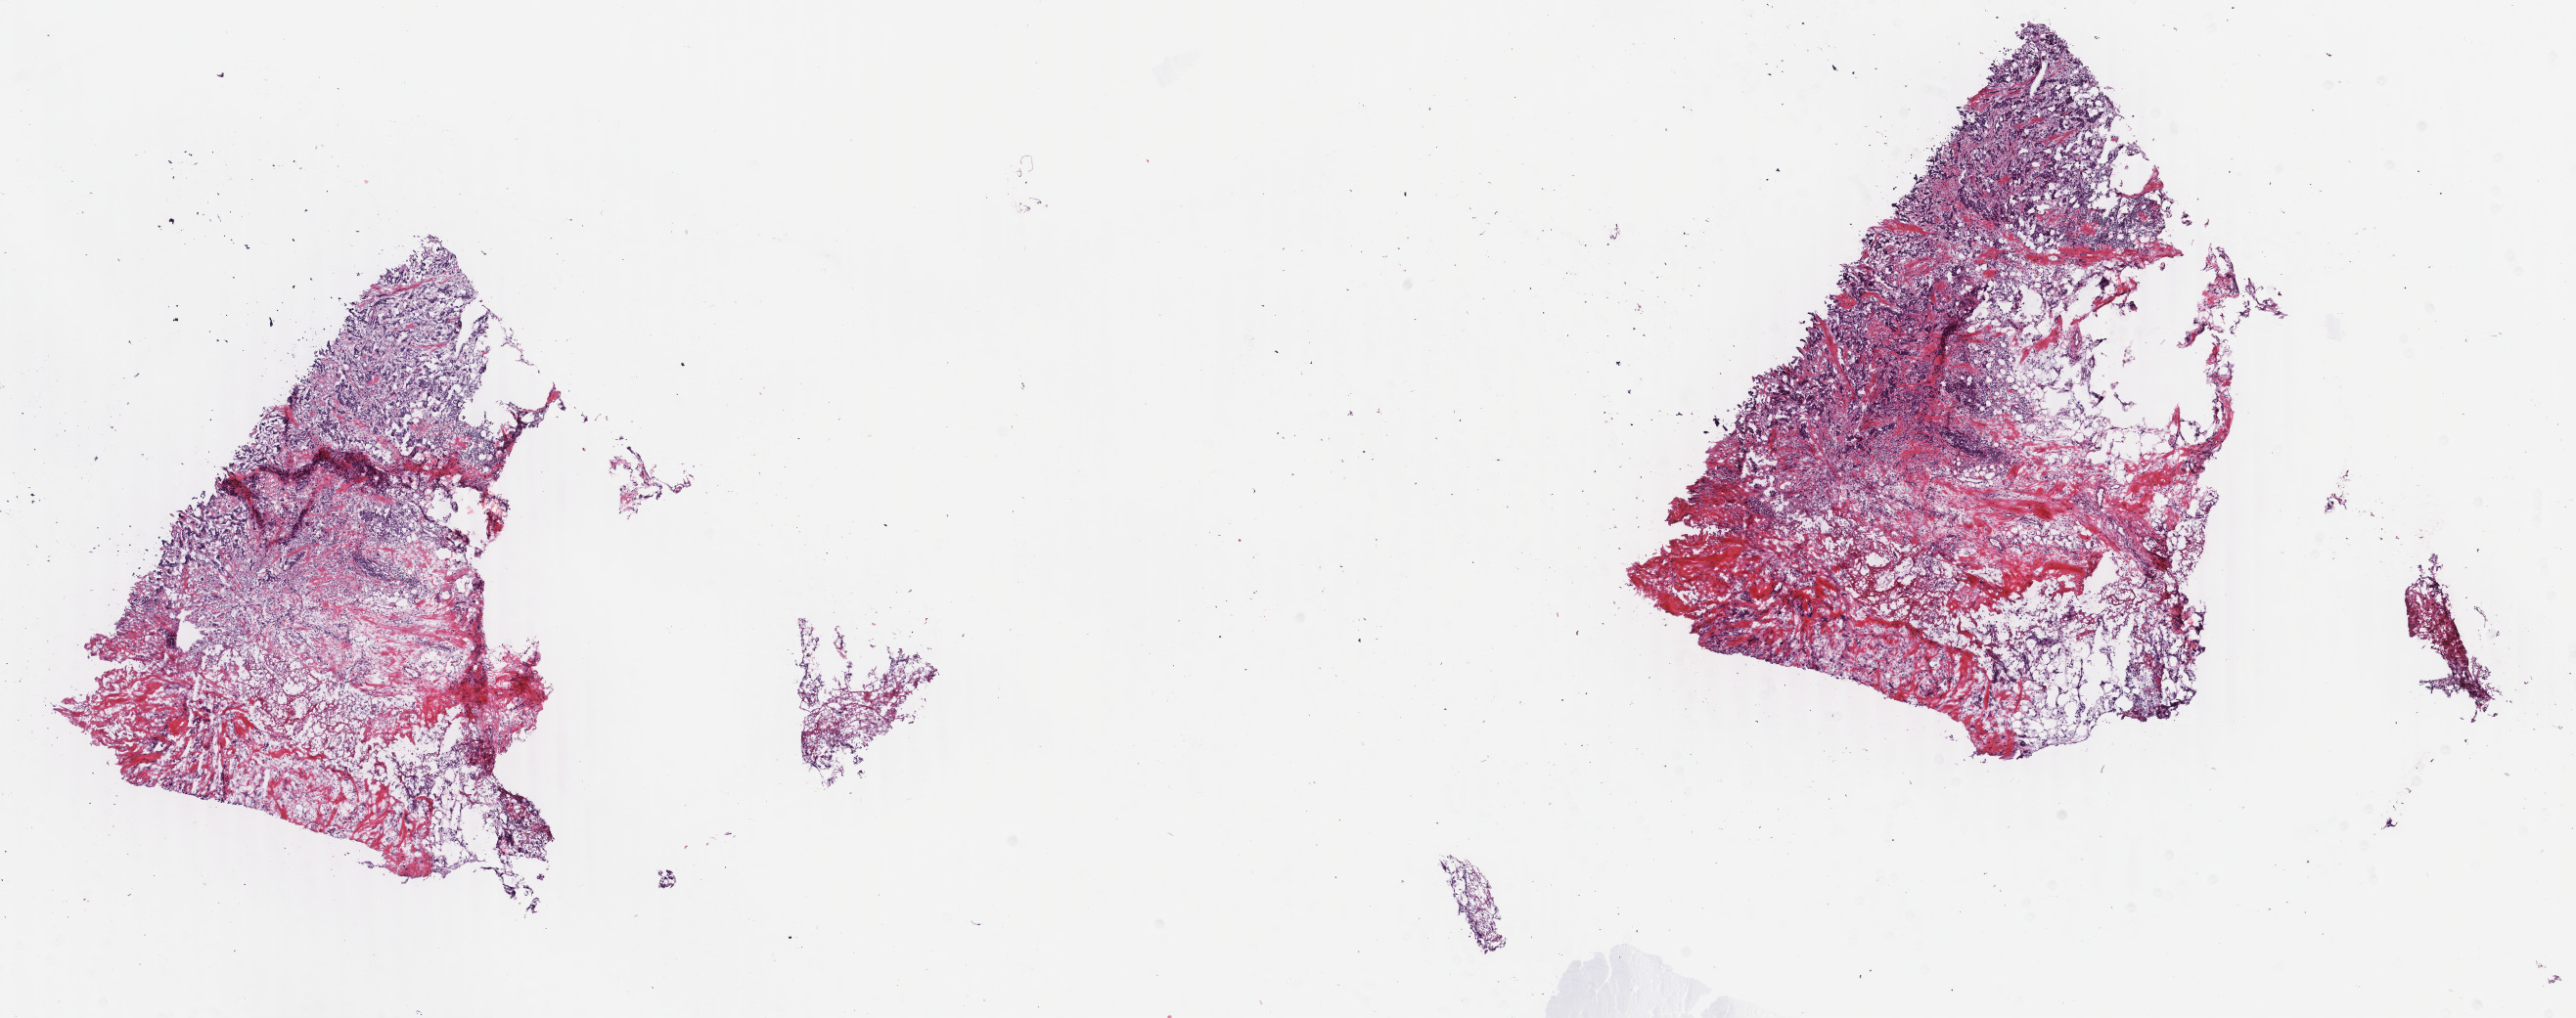
Digitized Hematoxylin and eosin (H&E) stained tissue section (whole slide) — a low-resolution overview of the entire scanned area, about 20.9 x 8.3 mm. Frozen section from the top of the tissue portion. Breast, primary tumour sample. Female patient; age at initial diagnosis 59 years. Slide review estimates, as recorded: tumour cells 70%, tumour nuclei 70%, normal cells 0%, stromal cells 30%, necrosis 0%. Infiltration values recorded for this section: lymphocyte infiltration 3%, monocyte infiltration 2%, neutrophil infiltration 1%.
Laterality: left. AJCC pathologic stage: IIB (6th edition). Diagnosis: Infiltrating duct carcinoma, NOS.